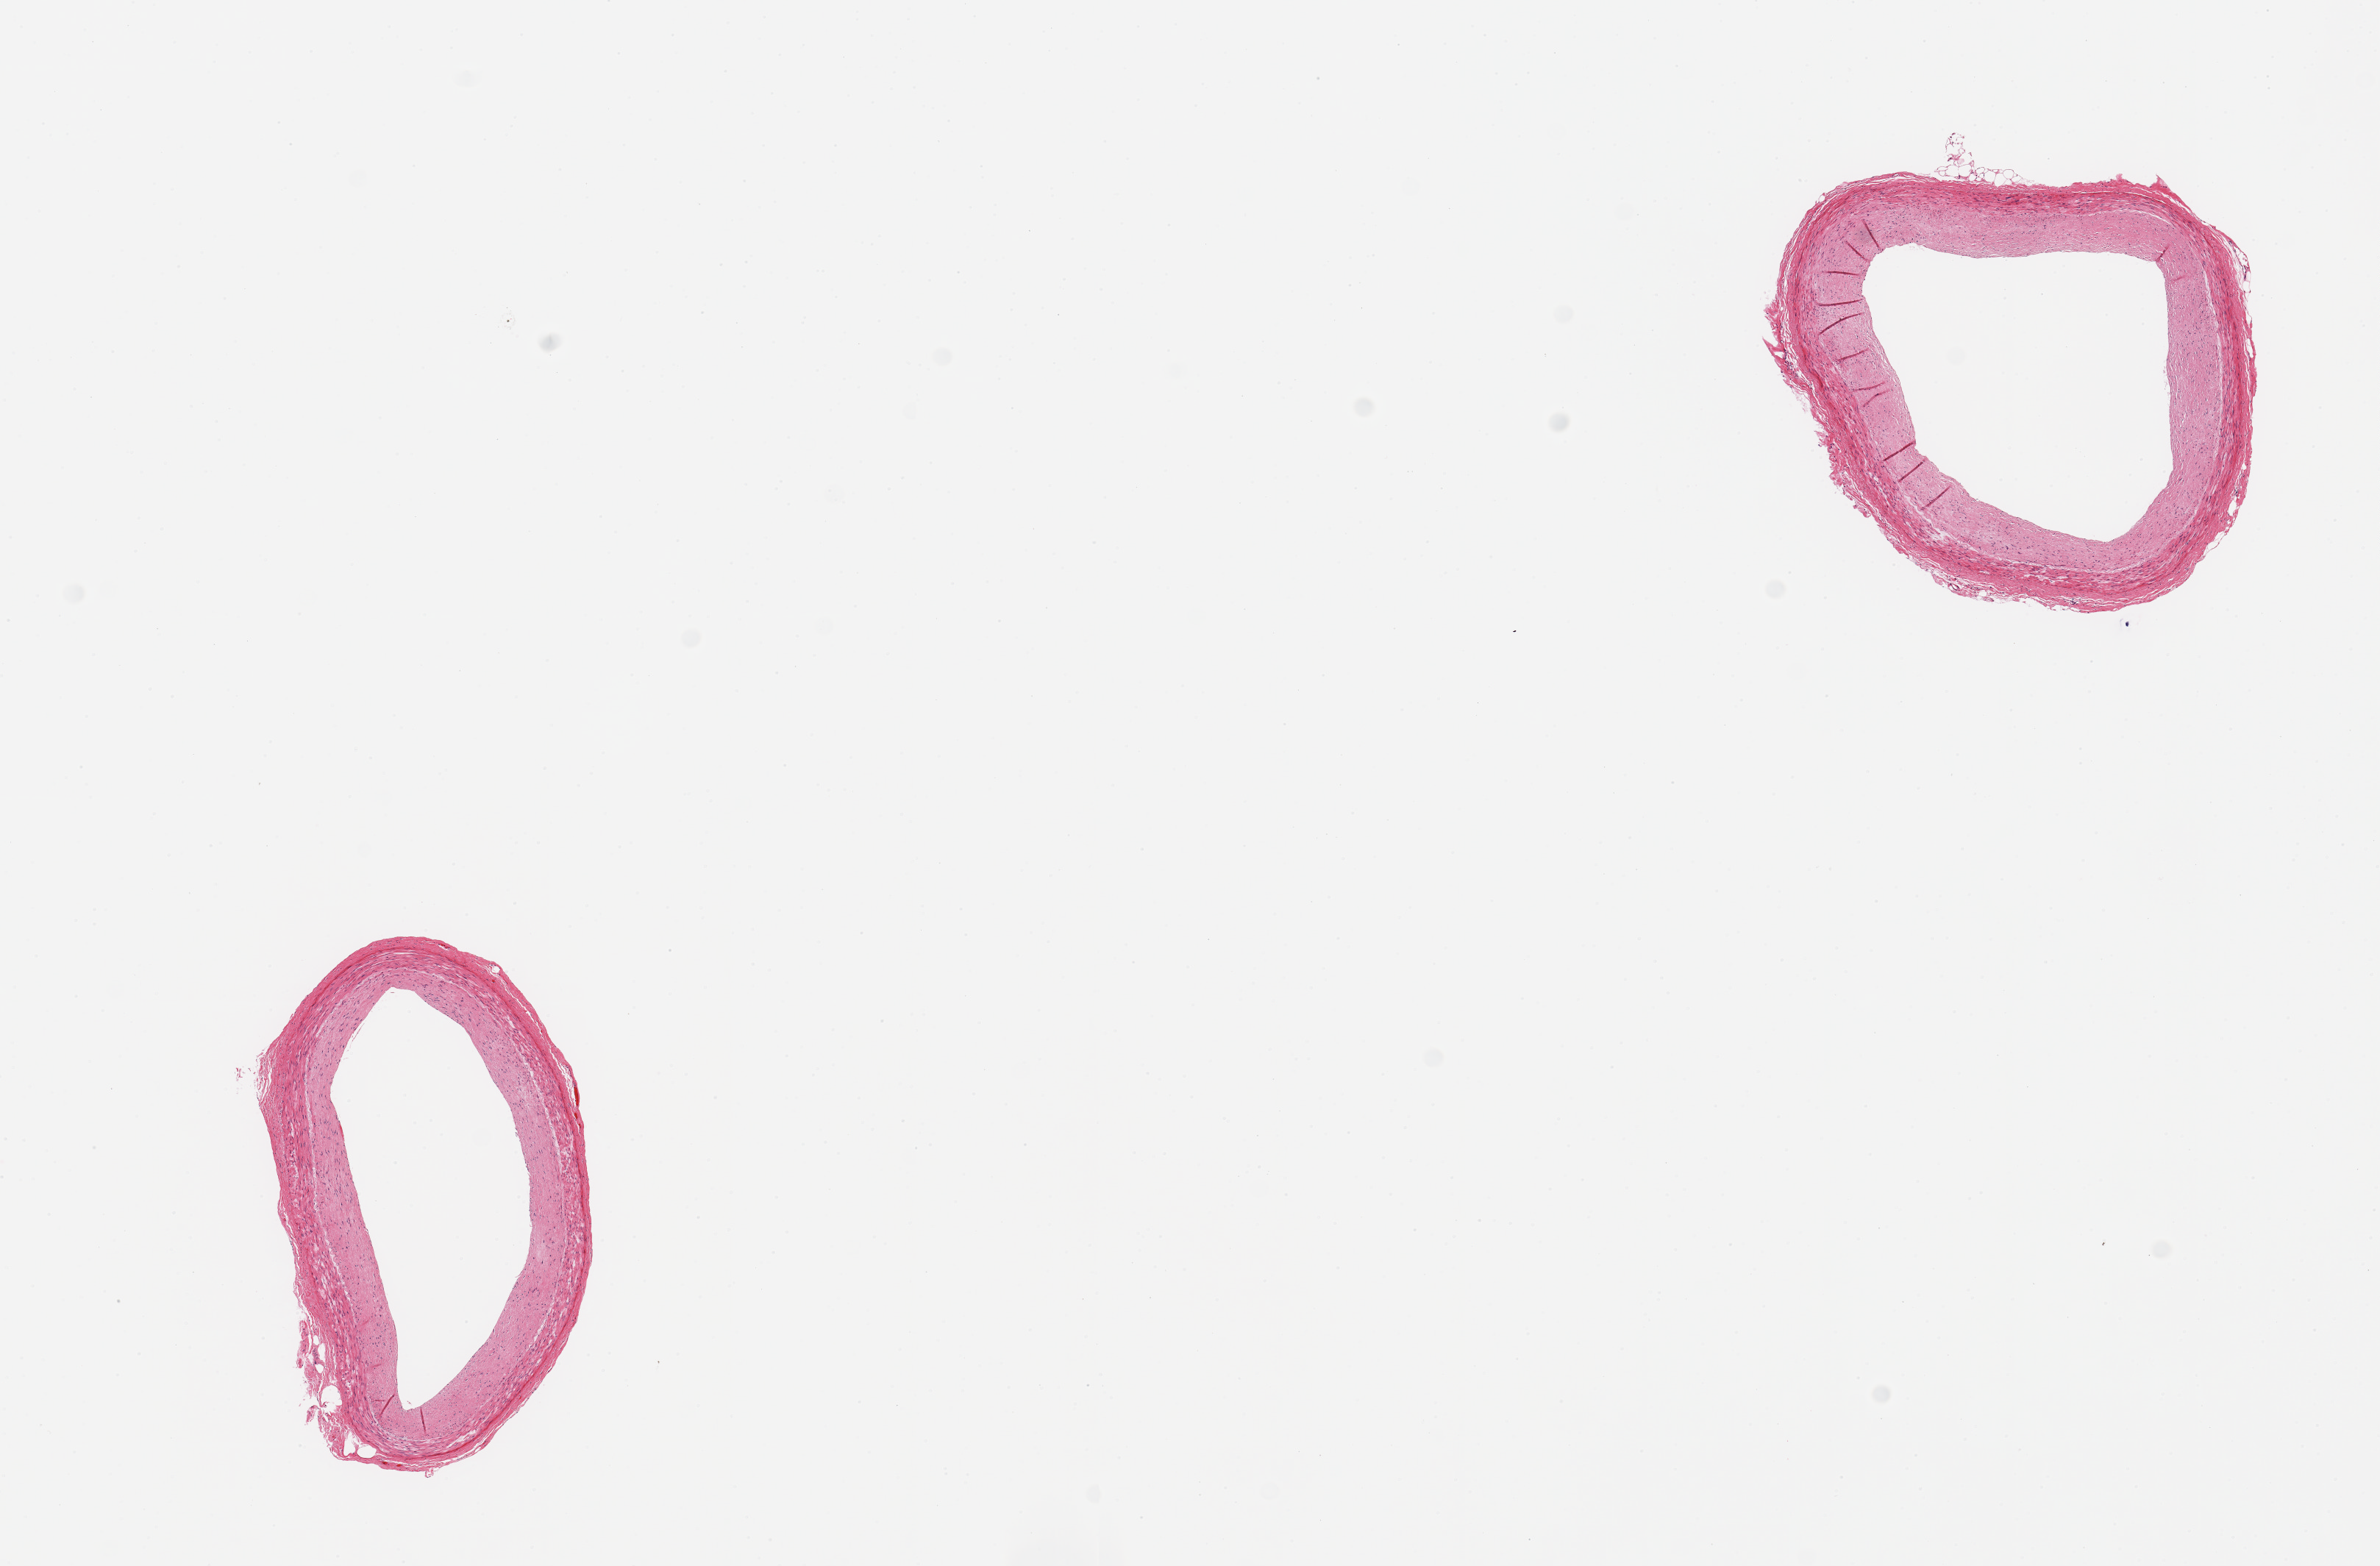
Whole-slide image, haematoxylin and eosin stain, brightfield, low-resolution overview of the scanned area, about 12.8 x 8.4 mm (acquisition: 20x scan). PAXgene-fixed paraffin-embedded (PFPE) section. Section of coronary artery (target tissue). Tissue donor sample.
Pathologist's review note for this sample: 2 pieces, no adherent fat or significant atherosis.